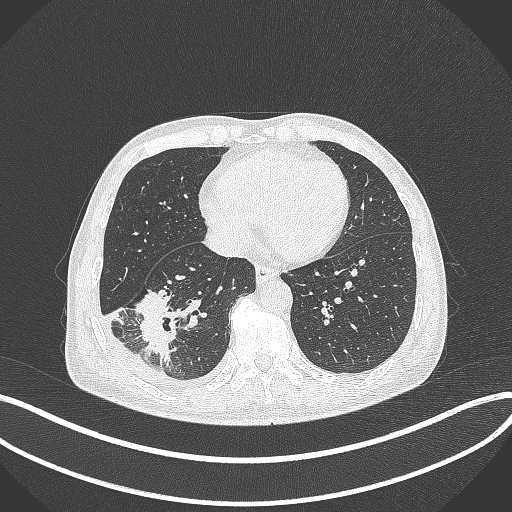
Chest CT, one axial slice; slice 126 of 388 in the series (ordered by position); reconstruction kernel B70f; lung window (W 1500 / L -600 HU); 1 mm slice thickness; 512 × 512 image matrix. Patient: male, 64 years. Case-level facts recorded for this patient, not image findings: clinical TNM (as recorded): T3 N0 M0.
Outlined on this slice (bounding box drawn by a radiologist):
- lung tumour (recorded histology: adenocarcinoma): bounding box <127,286,185,370> (left, top, right, bottom; pixels)